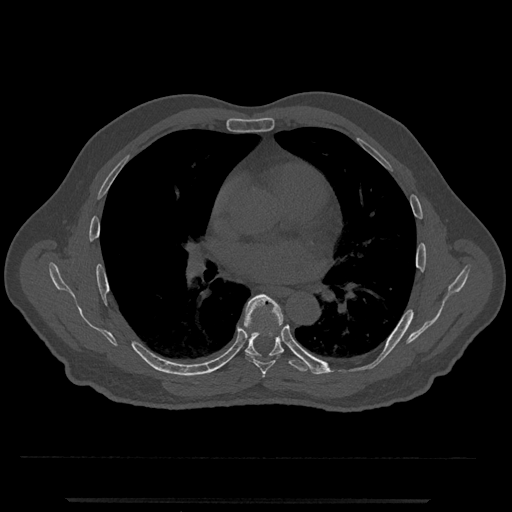
CT including the spine, one axial slice; slice 713 of 797 in the series (ordered by position); bone window (W 1800 / L 400 HU); 0.5 mm slice thickness; 512 × 512 image matrix, field of view 419 × 419 mm. Male patient, age 63 years. From the clinical record (not read from this slice): primary cancer: prostate.
Annotated regions visible in this slice (semi-automatic segmentation, software-assisted and operator-edited):
- T5 vertebra: bounding box [x1, y1, x2, y2] px = [262, 374, 265, 377]
- T6 vertebra: [244, 294, 283, 374]
- T7 vertebra: [221, 294, 321, 375]